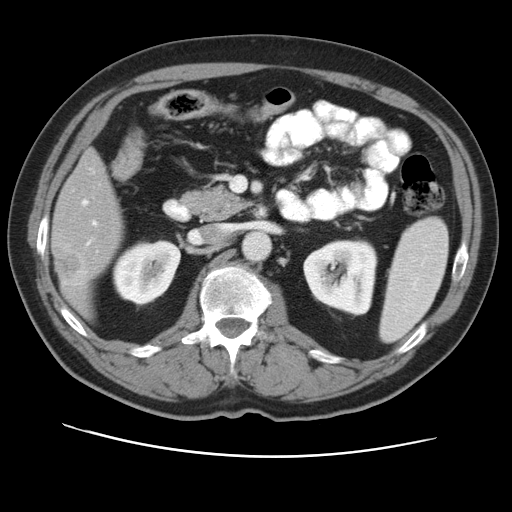
Contrast-enhanced abdominal CT, one axial slice; position 20 of 49 along the scan axis; reconstruction kernel STANDARD; intravenous contrast given; soft-tissue window (W 400 / L 40 HU); 5 mm slice thickness; 512 × 512 image matrix. Male patient, age 59 years. From the clinical record (not read from this slice): diagnosis: colorectal cancer liver metastases, imaged before liver resection.
Annotated regions visible in this slice (outlined manually by an expert reader):
- hepatic veins: box from (x=82, y=200) to (x=87, y=205) px
- liver: (x=54, y=153)–(x=122, y=312)
- planned liver remnant (the part of the liver to remain after resection): (x=59, y=153)–(x=122, y=241)
- portal vein (with intrahepatic branches): (x=88, y=221)–(x=97, y=244)
- liver metastasis: (x=54, y=248)–(x=82, y=283)